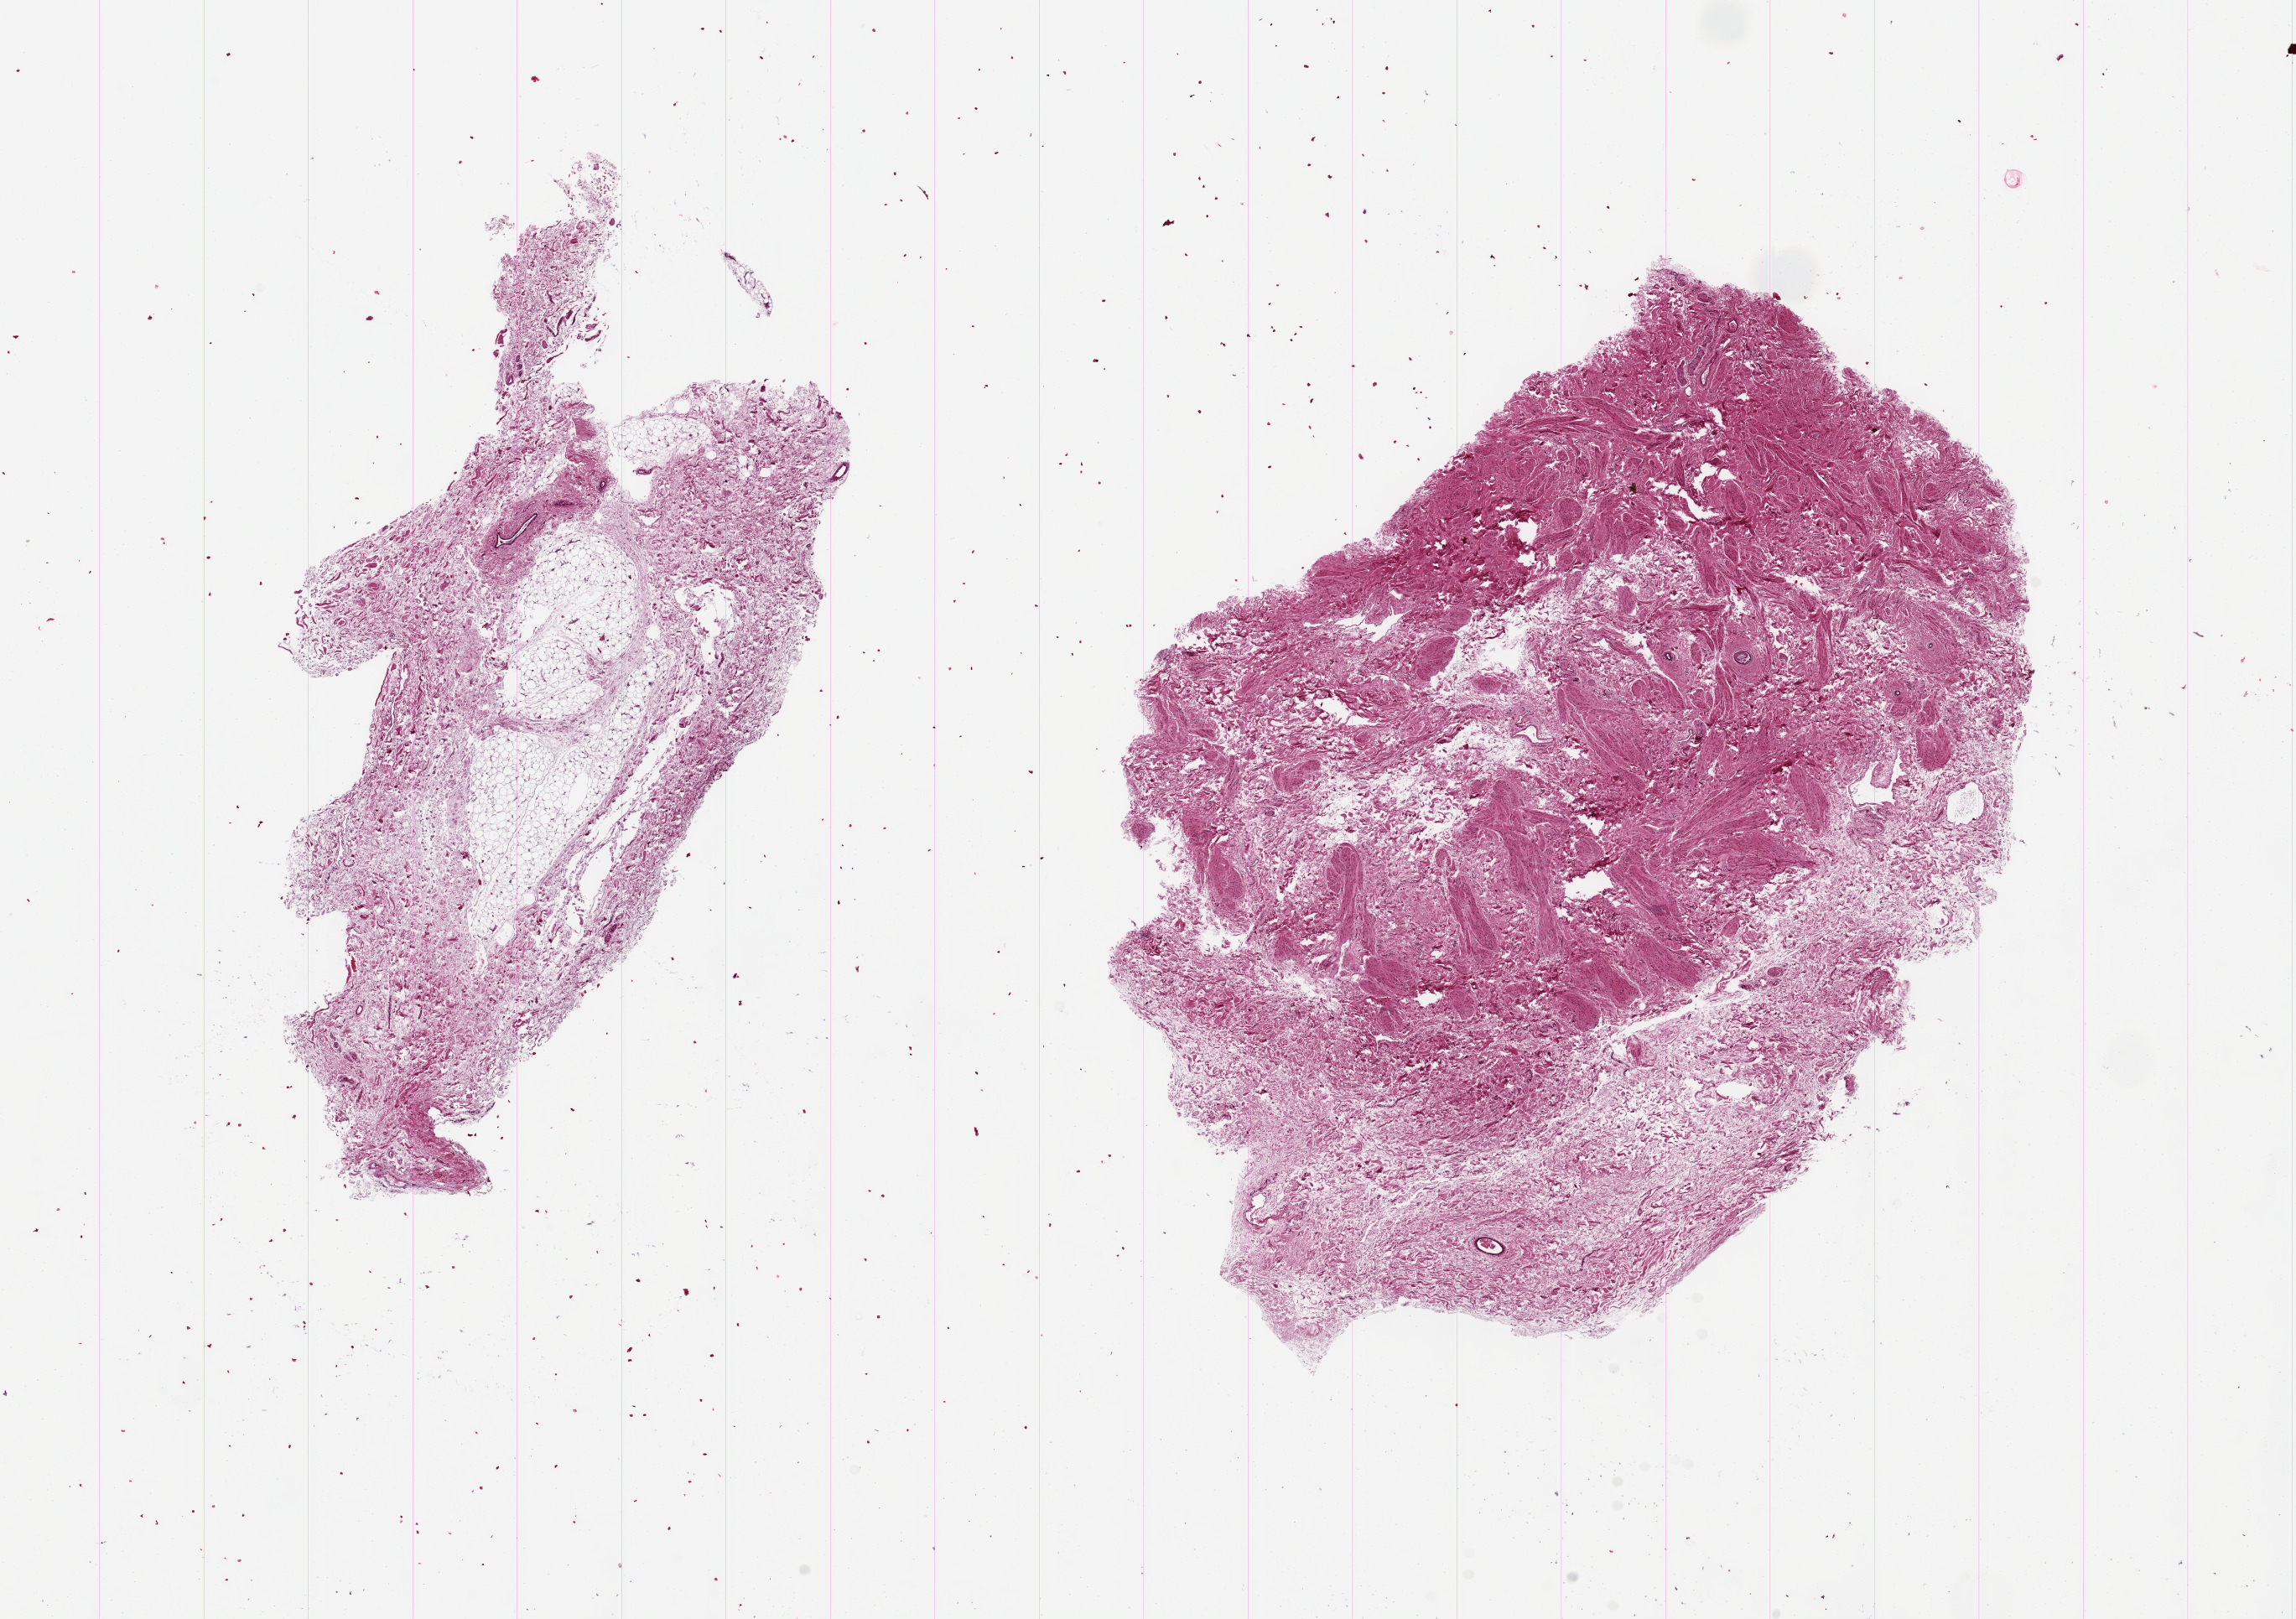
Whole-slide image, H&E stain, whole scanned area (about 21.7 x 15.3 mm, slide scanned at 20x) shown as a low-resolution overview. PAXgene-fixed paraffin-embedded (PFPE) section. Target tissue: breast. Donor tissue sample. Female donor.
• pathologist's review note for this sample: 2 ~9x6mm aliquots, few atrophic ductal structures; one aliquot with extensive ???contaminating??? skeletal muscle (?pectoralis)